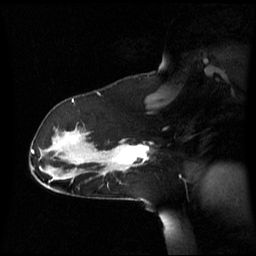
Breast MRI (dynamic contrast-enhanced), one sagittal slice; position 40 of 60 along the scan axis; dynamic contrast-enhanced series, image 2 of 3 at this slice position (ordered by acquisition); 1.5 T; TE 4.2 ms, TR 8.4 ms; 256 × 256 image matrix. Female patient, age 39 years. From the clinical record (not read from this slice): setting: breast cancer imaged before/during neoadjuvant chemotherapy; receptor status: triple-negative.
Structures marked on this image (semi-automatically segmented with operator editing):
- analysis volume of interest (the breast-tissue region the enhancement analysis was run in; not a lesion): bounding box <101,140,149,173> (left, top, right, bottom; pixels)
- tumour enhancement mask (voxels above the 70 % enhancement threshold inside the analysis volume of interest): <116,145,149,164>